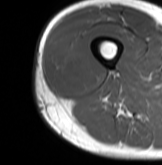
MRI of an extremity soft-tissue mass, one axial slice; slice 23 of 61 in the series (ordered by position); MR volume resampled by the dataset authors to the PET/CT grid (not the native acquisition matrix); 3.27 mm slice thickness; 162 × 165 image matrix. Male patient. Case-level facts recorded for this patient, not image findings: histological type: poorly differentiated synovial sarcoma; grade: high; site of the primary tumour: right buttock.
Annotated regions visible in this slice (expert contour drawn on MRI and transferred to this co-registered scan by the dataset authors):
- gross tumour volume including surrounding oedema: bounding box [x1, y1, x2, y2] px = [52, 40, 99, 96]
- gross tumour volume (mass): [55, 45, 78, 89]